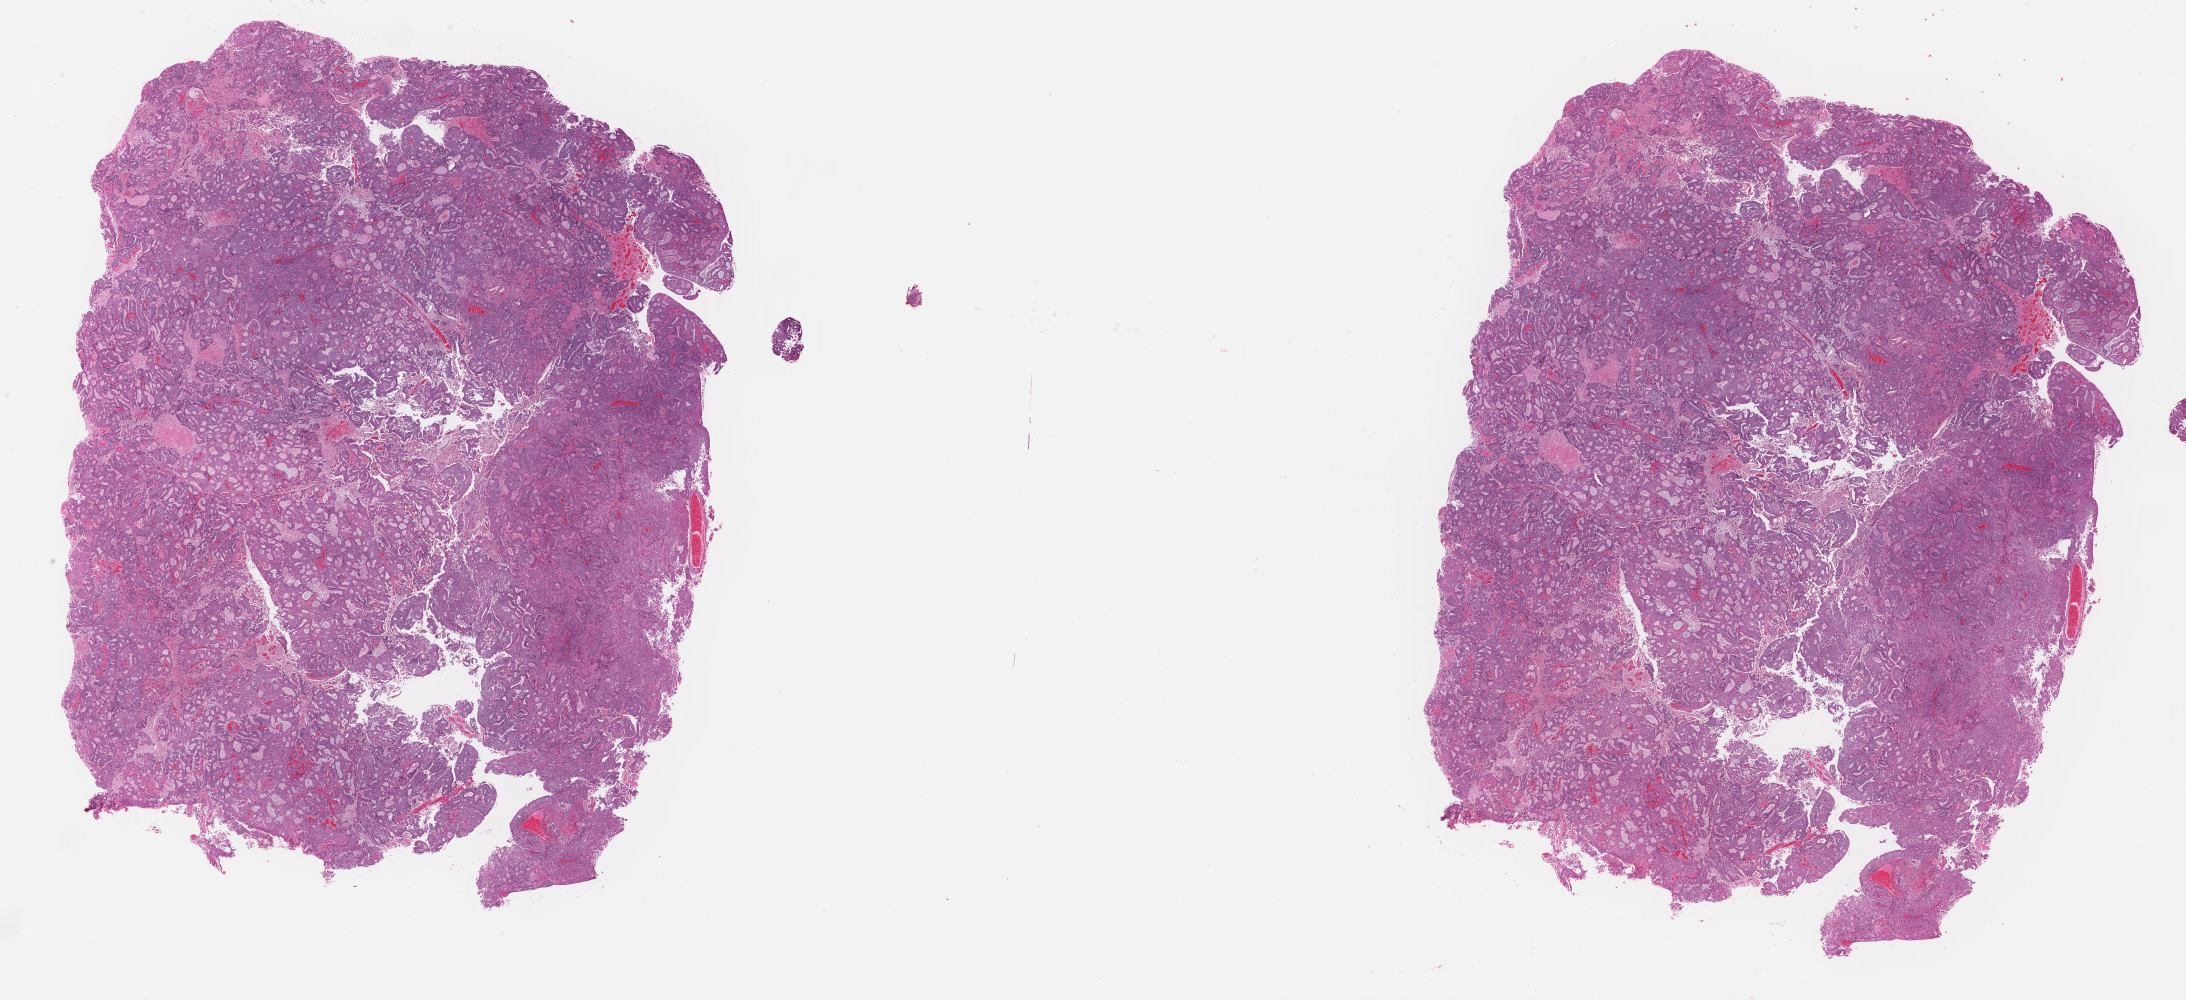
Digitized H&E tissue section (whole slide), a low-resolution overview of the entire scanned area, about 34.5 x 15.8 mm; formalin-fixed paraffin-embedded (FFPE) diagnostic section; primary tumour sample from the uterus. Female, age 73 years at initial diagnosis. Histologic grade: G3 (poorly differentiated).
* FIGO stage: IVB
* pathologic diagnosis: Endometrioid adenocarcinoma, NOS (endometrium)